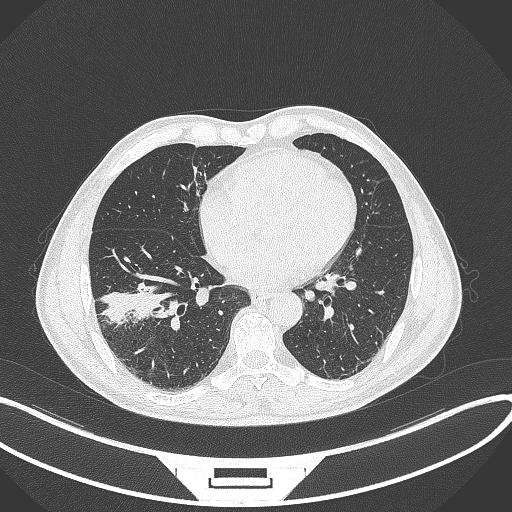
Chest CT, one axial slice; slice 140 of 364 in the series (ordered by position); lung window (W 1500 / L -600 HU); 512 × 512 image matrix. Male patient, age 58 years. Case-level facts recorded for this patient, not image findings: clinical TNM (as recorded): T3 N0 M0.
Outlined on this slice (bounding box drawn by a radiologist):
- lung tumour (recorded histology: squamous cell carcinoma): bounding box (x1, y1, x2, y2) in pixels: (96, 290, 163, 328)